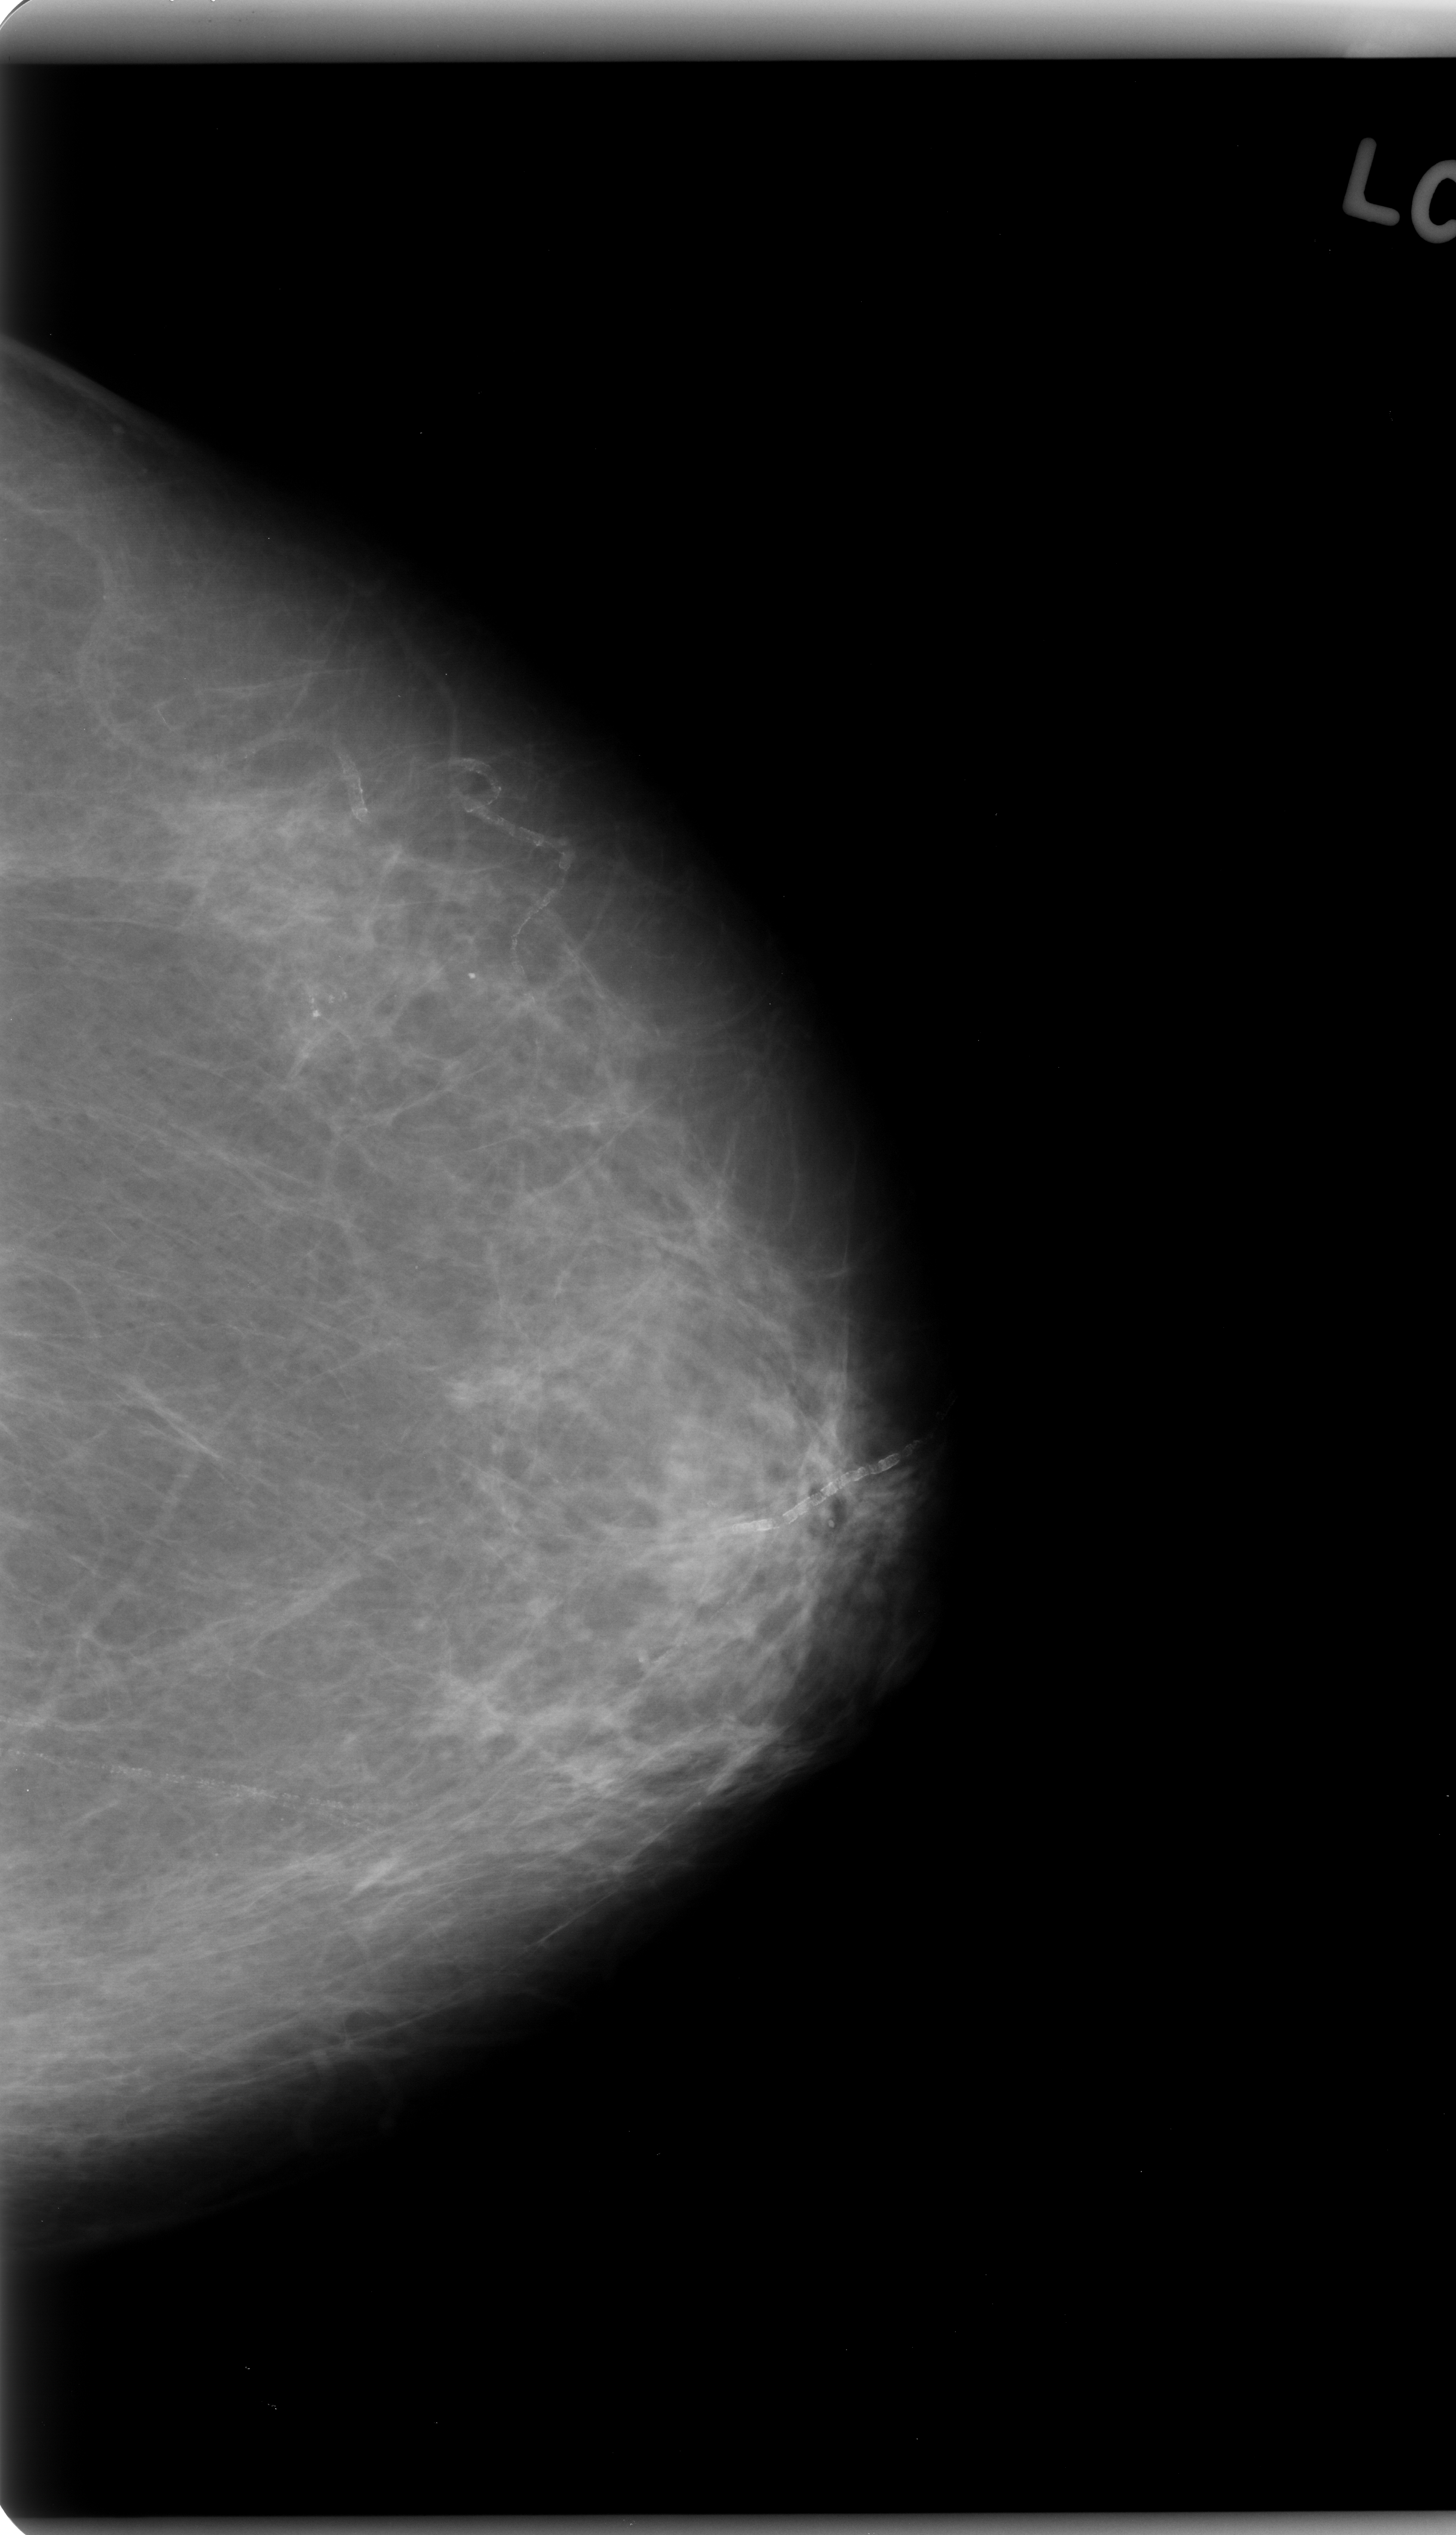
Mammogram (digitized film), left breast, craniocaudal (CC) view, BI-RADS breast density category 1 (scale 1–4).
Finding: calcifications, morphology pleomorphic, distribution clustered; BI-RADS assessment category 4; pathology result (as recorded, not read from the image): benign.